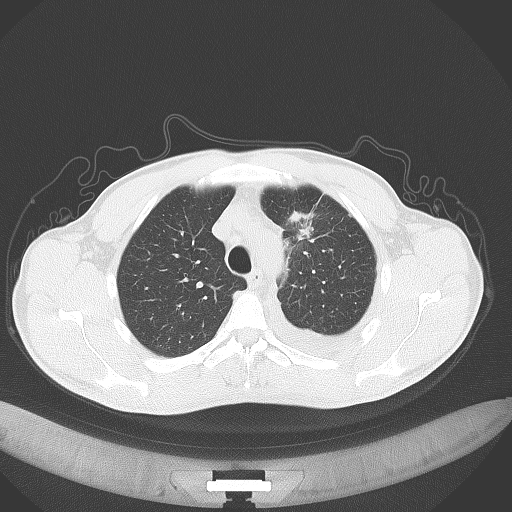
Chest CT, one axial slice; position 103 of 130 along the scan axis; reconstruction kernel B70f; lung window (W 1500 / L -600 HU); 3 mm slice thickness; 512 × 512 image matrix, field of view 400 × 400 mm. Patient: male, 49 years. Case-level facts recorded for this patient, not image findings: clinical TNM (as recorded): T1c N1 M1.
Outlined on this slice (bounding box drawn by a radiologist):
- lung tumour (recorded histology: adenocarcinoma): bounding box <287,207,324,246> (left, top, right, bottom; pixels)